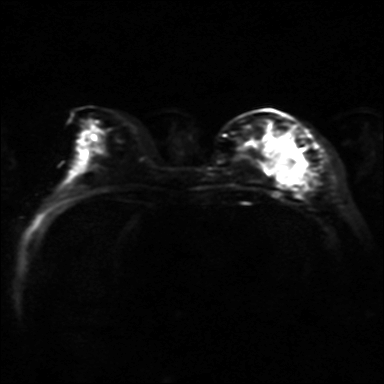
Breast MRI, one axial slice. Slice 13 of 36 in the series (ordered by position). Diffusion-weighted series; image 2 of 4 stored at this slice position (different b-values; order by instance number). 3 T. 4 mm slice thickness. 384 × 384 image matrix. Female patient.
Structures marked on this image (outlined manually by an expert reader):
- tumour on diffusion-weighted imaging: bounding box (x1, y1, x2, y2) in pixels: (274, 147, 305, 184)